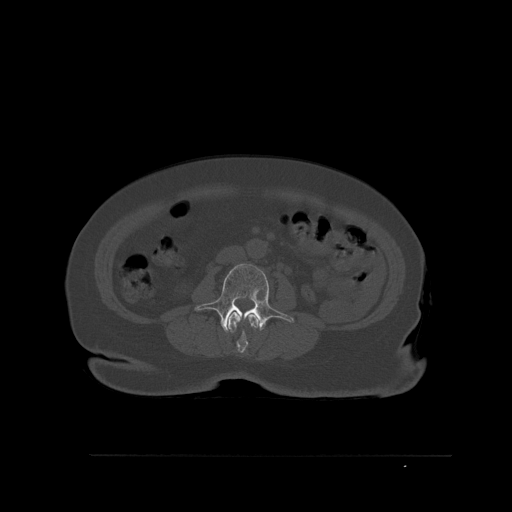
CT including the spine, one axial slice. Slice 230 of 527 in the series (ordered by position). Bone window (W 1800 / L 400 HU). 1.5 mm slice thickness. 512 × 512 image matrix. Patient: female, 73 years. From the clinical record (not read from this slice): primary cancer: breast.
Structures marked on this image (semi-automatic segmentation, software-assisted and operator-edited):
- L2 vertebra: box from (x=227, y=312) to (x=259, y=353) px
- L3 vertebra: (x=194, y=263)–(x=294, y=333)